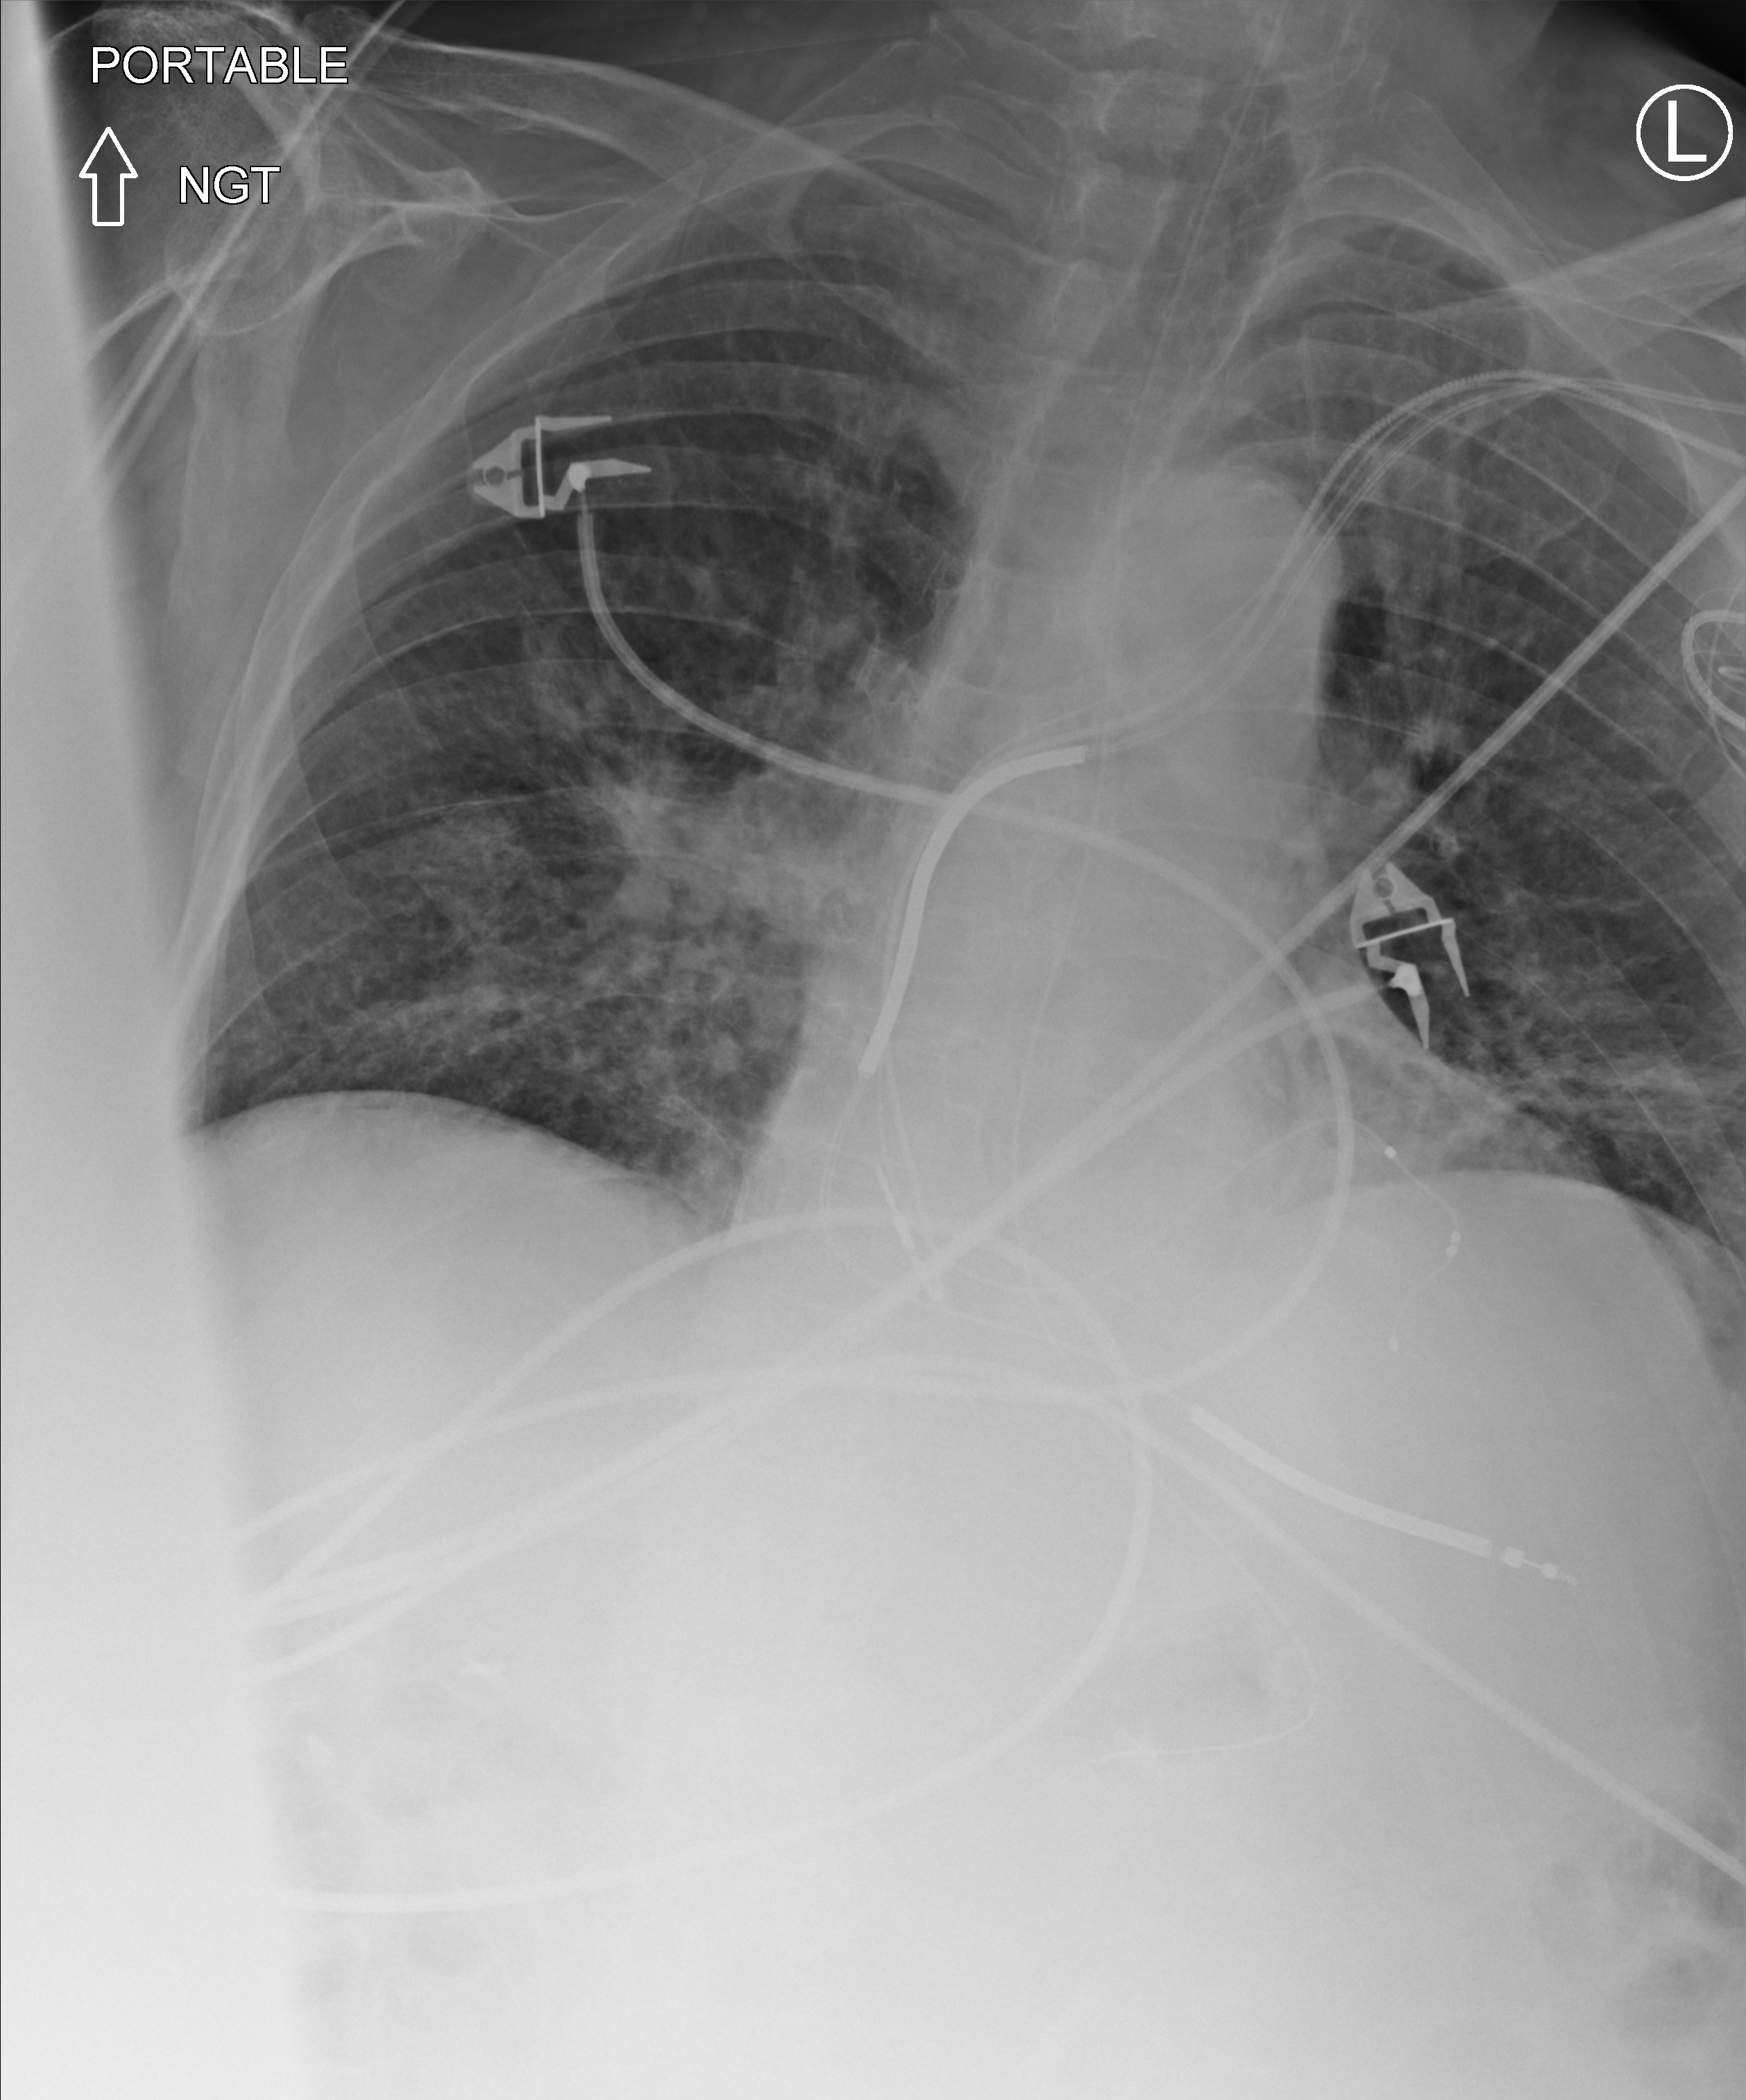
Bedside chest radiograph (computed radiography); anteroposterior (AP) projection. Male patient hospitalised with COVID-19, age 75–90 years.
Hospital-stay facts (about this admission, not read from this image; timing relative to this image not recorded):
- admitted to intensive care during this hospital stay: no
- length of hospital stay: 4 days